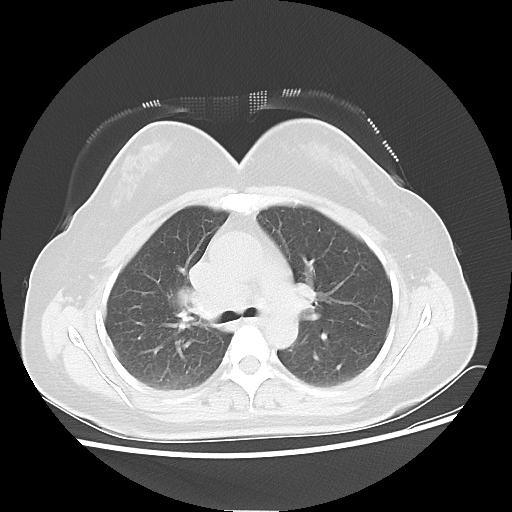
Chest CT, one axial slice. Position 33 of 50 along the scan axis. 100 kVp. Lung window (W 1500 / L -600 HU). 5 mm slice thickness. 512 × 512 image matrix, field of view 360 × 360 mm. Female patient, age 40 years. From the clinical record (not read from this slice): clinical TNM (as recorded): T1c N3 M0; histopathological grade: G3.
Annotated regions visible in this slice (rectangle marked by the reading radiologist):
- lung tumour (recorded histology: small cell carcinoma): bounding box (x1, y1, x2, y2) in pixels: (165, 274, 200, 320)